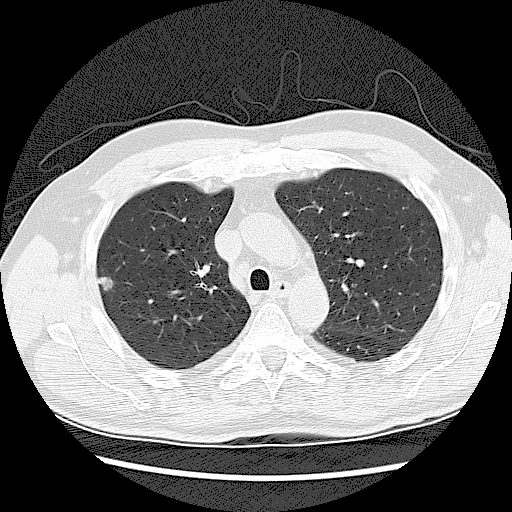
Low-dose screening chest CT, one axial slice; position 84 of 120 along the scan axis; reconstruction kernel LUNG; 120 kVp; lung window (W 1500 / L -600 HU); 2.5 mm slice thickness; 512 × 512 image matrix, field of view 360 × 360 mm.
Outlined on this slice (expert manual segmentation):
- lesion 1 (tumor, upper lobe of right lung): bounding box (x1, y1, x2, y2) in pixels: (99, 269, 117, 291)